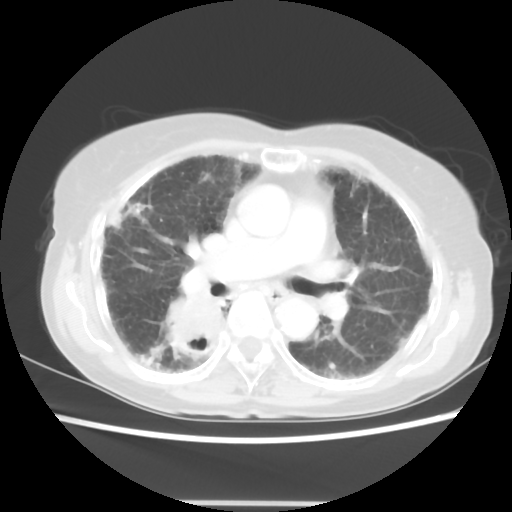
Chest CT, one axial slice; position 30 of 52 along the scan axis; 120 kVp; lung window (W 1500 / L -600 HU); 5 mm slice thickness; 512 × 512 image matrix, field of view 325 × 325 mm. Female patient, age 71 years. Case-level facts recorded for this patient, not image findings: clinical TNM (as recorded): T3 N0 M0.
Outlined on this slice (rectangle marked by the reading radiologist):
- lung tumour (recorded histology: squamous cell carcinoma): bounding box (x1, y1, x2, y2) in pixels: (163, 293, 228, 366)